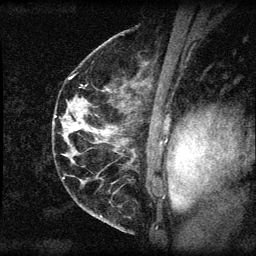
Breast MRI (dynamic contrast-enhanced), one sagittal slice. Dynamic contrast-enhanced series, image 2 of 3 at this slice position (ordered by acquisition). 1.5 T. TE 4.2 ms, TR 8.2 ms. 256 × 256 image matrix. Patient: female, 45 years.
Annotated regions visible in this slice (semi-automatic segmentation, software-assisted and operator-edited):
- analysis volume of interest (the breast-tissue region the enhancement analysis was run in; not a lesion): box from (x=55, y=110) to (x=94, y=148) px
- tumour enhancement mask (voxels above the 70 % enhancement threshold inside the analysis volume of interest): (x=55, y=116)–(x=81, y=131)